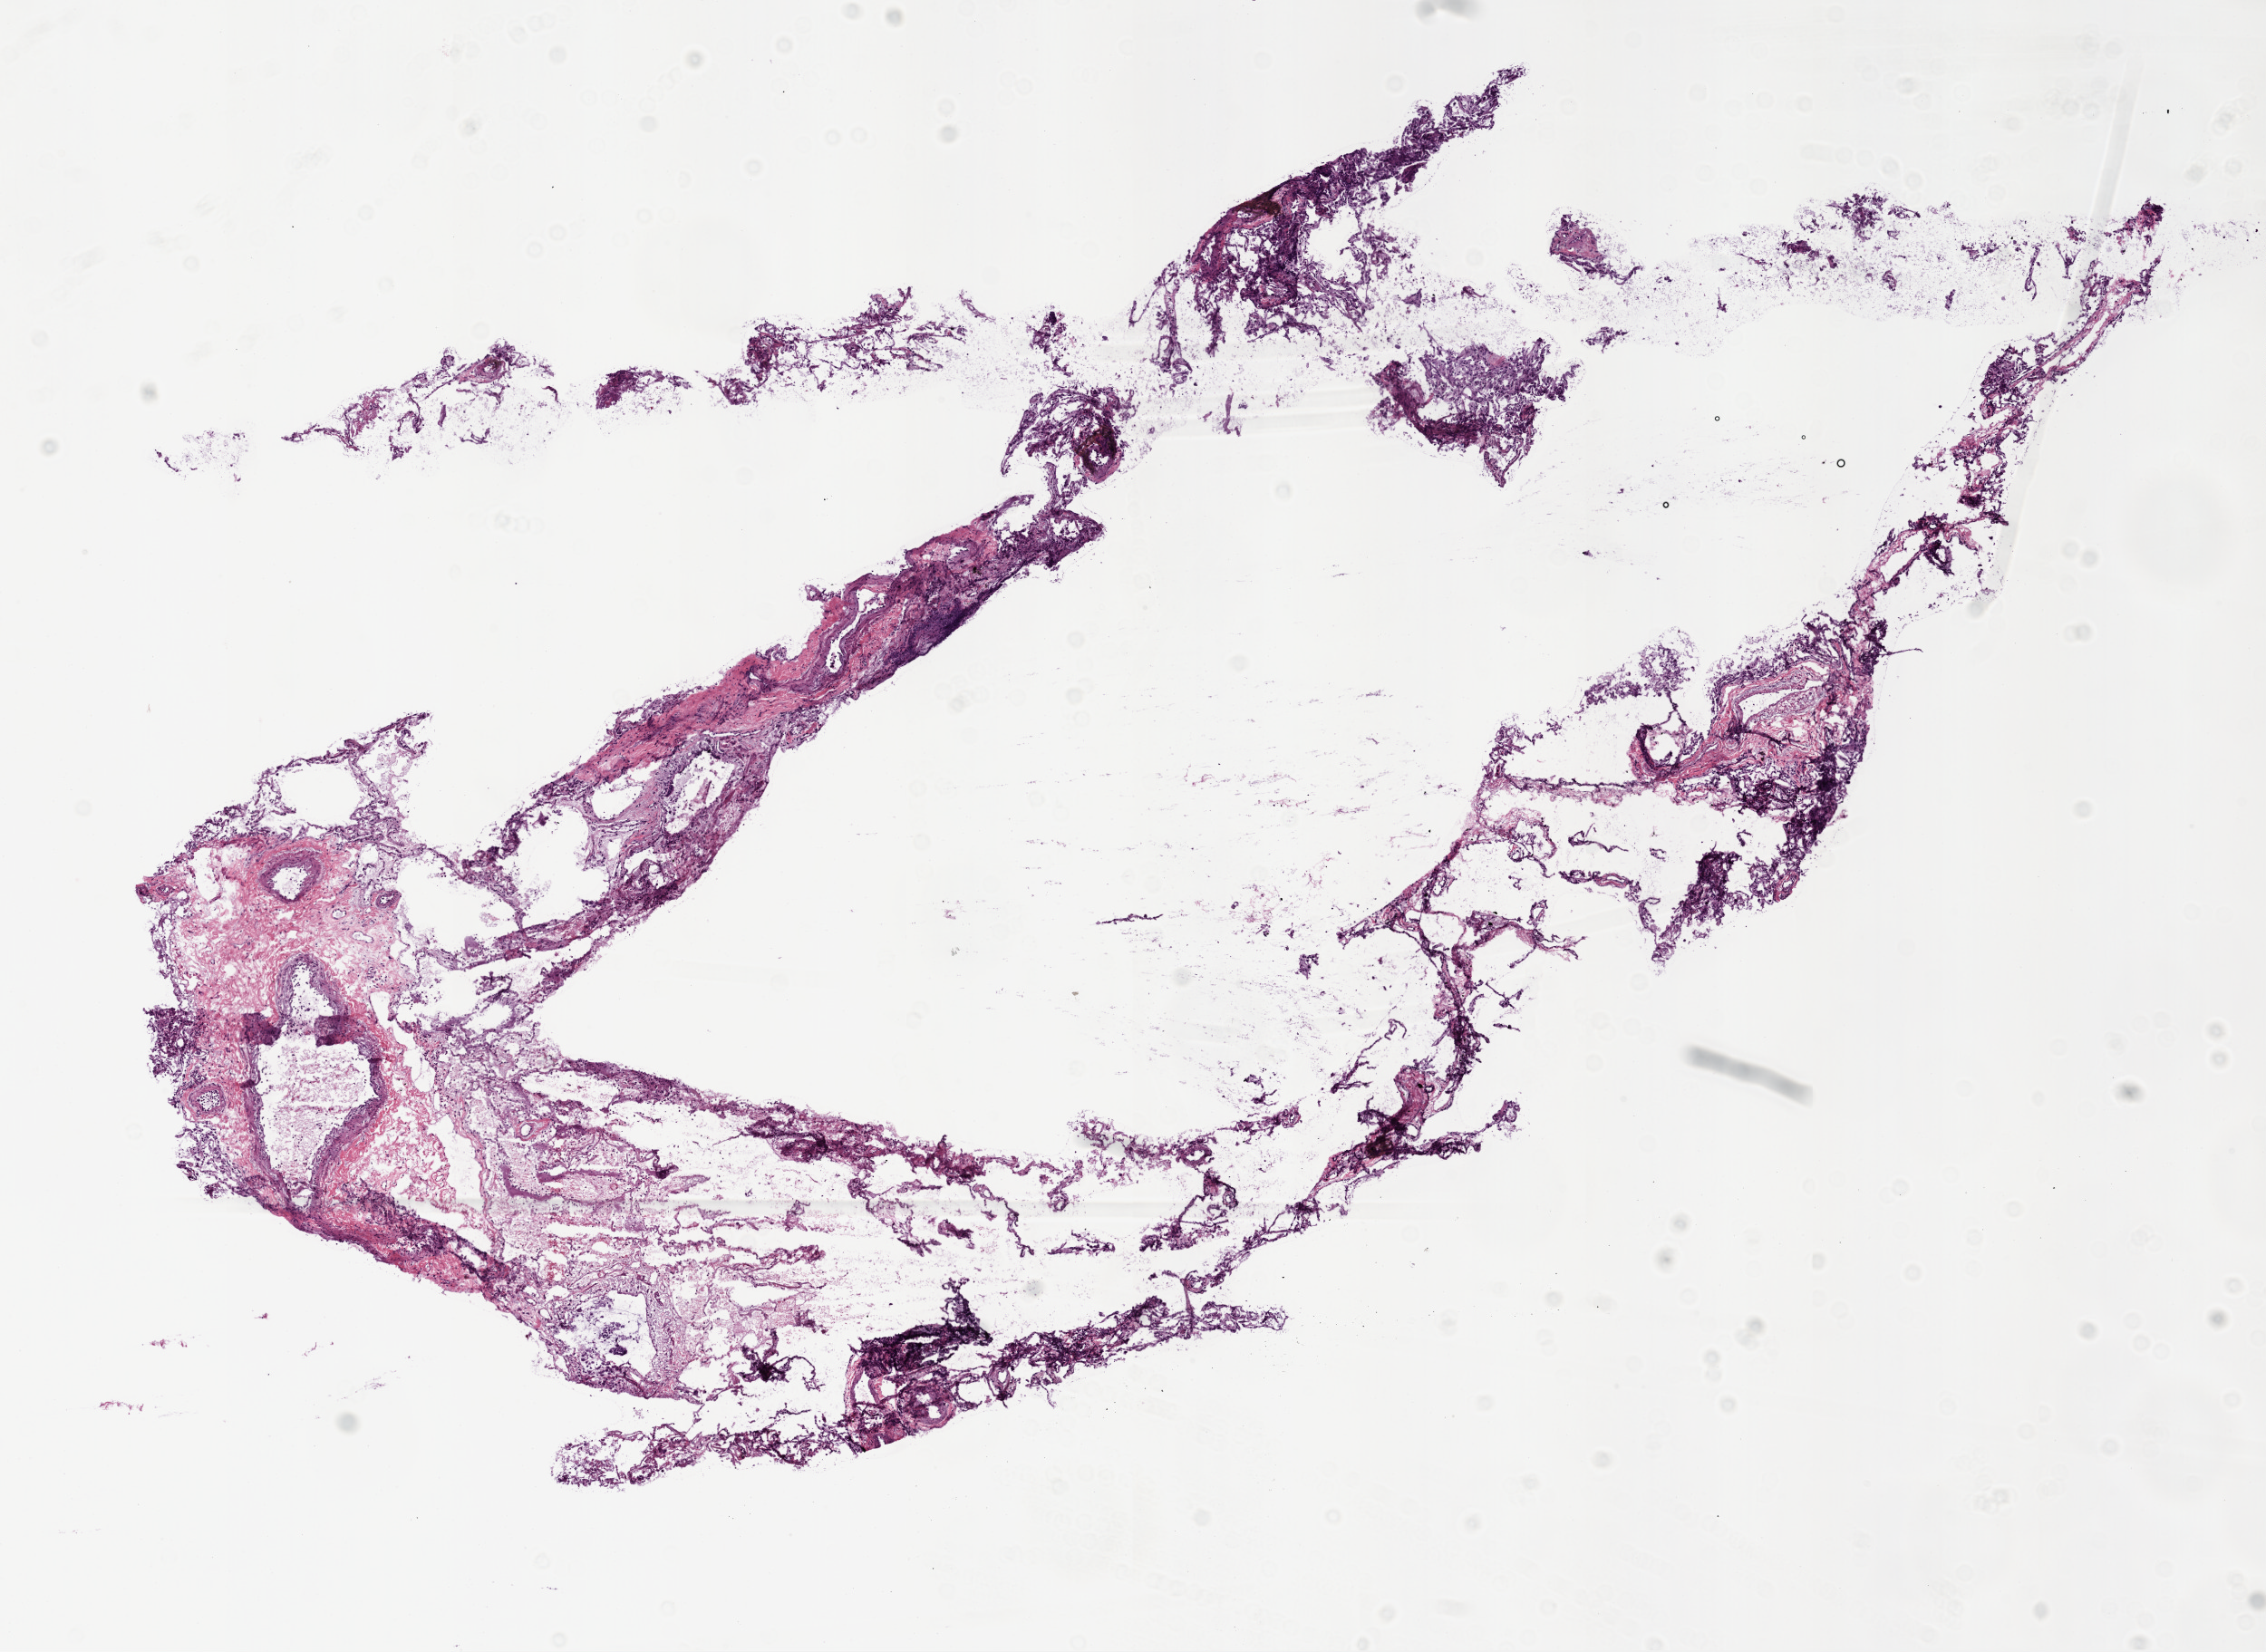
Whole-slide histology image, Hematoxylin and eosin (H&E) stained, low-resolution overview of the scanned area, about 10.0 x 7.3 mm, frozen section, solid tissue normal (non-tumour tissue) sample from the lung. Patient: female, age at initial diagnosis 74 years.
- this section: solid tissue normal sample (biorepository sample class)
- patient diagnosis: Squamous cell carcinoma, NOS